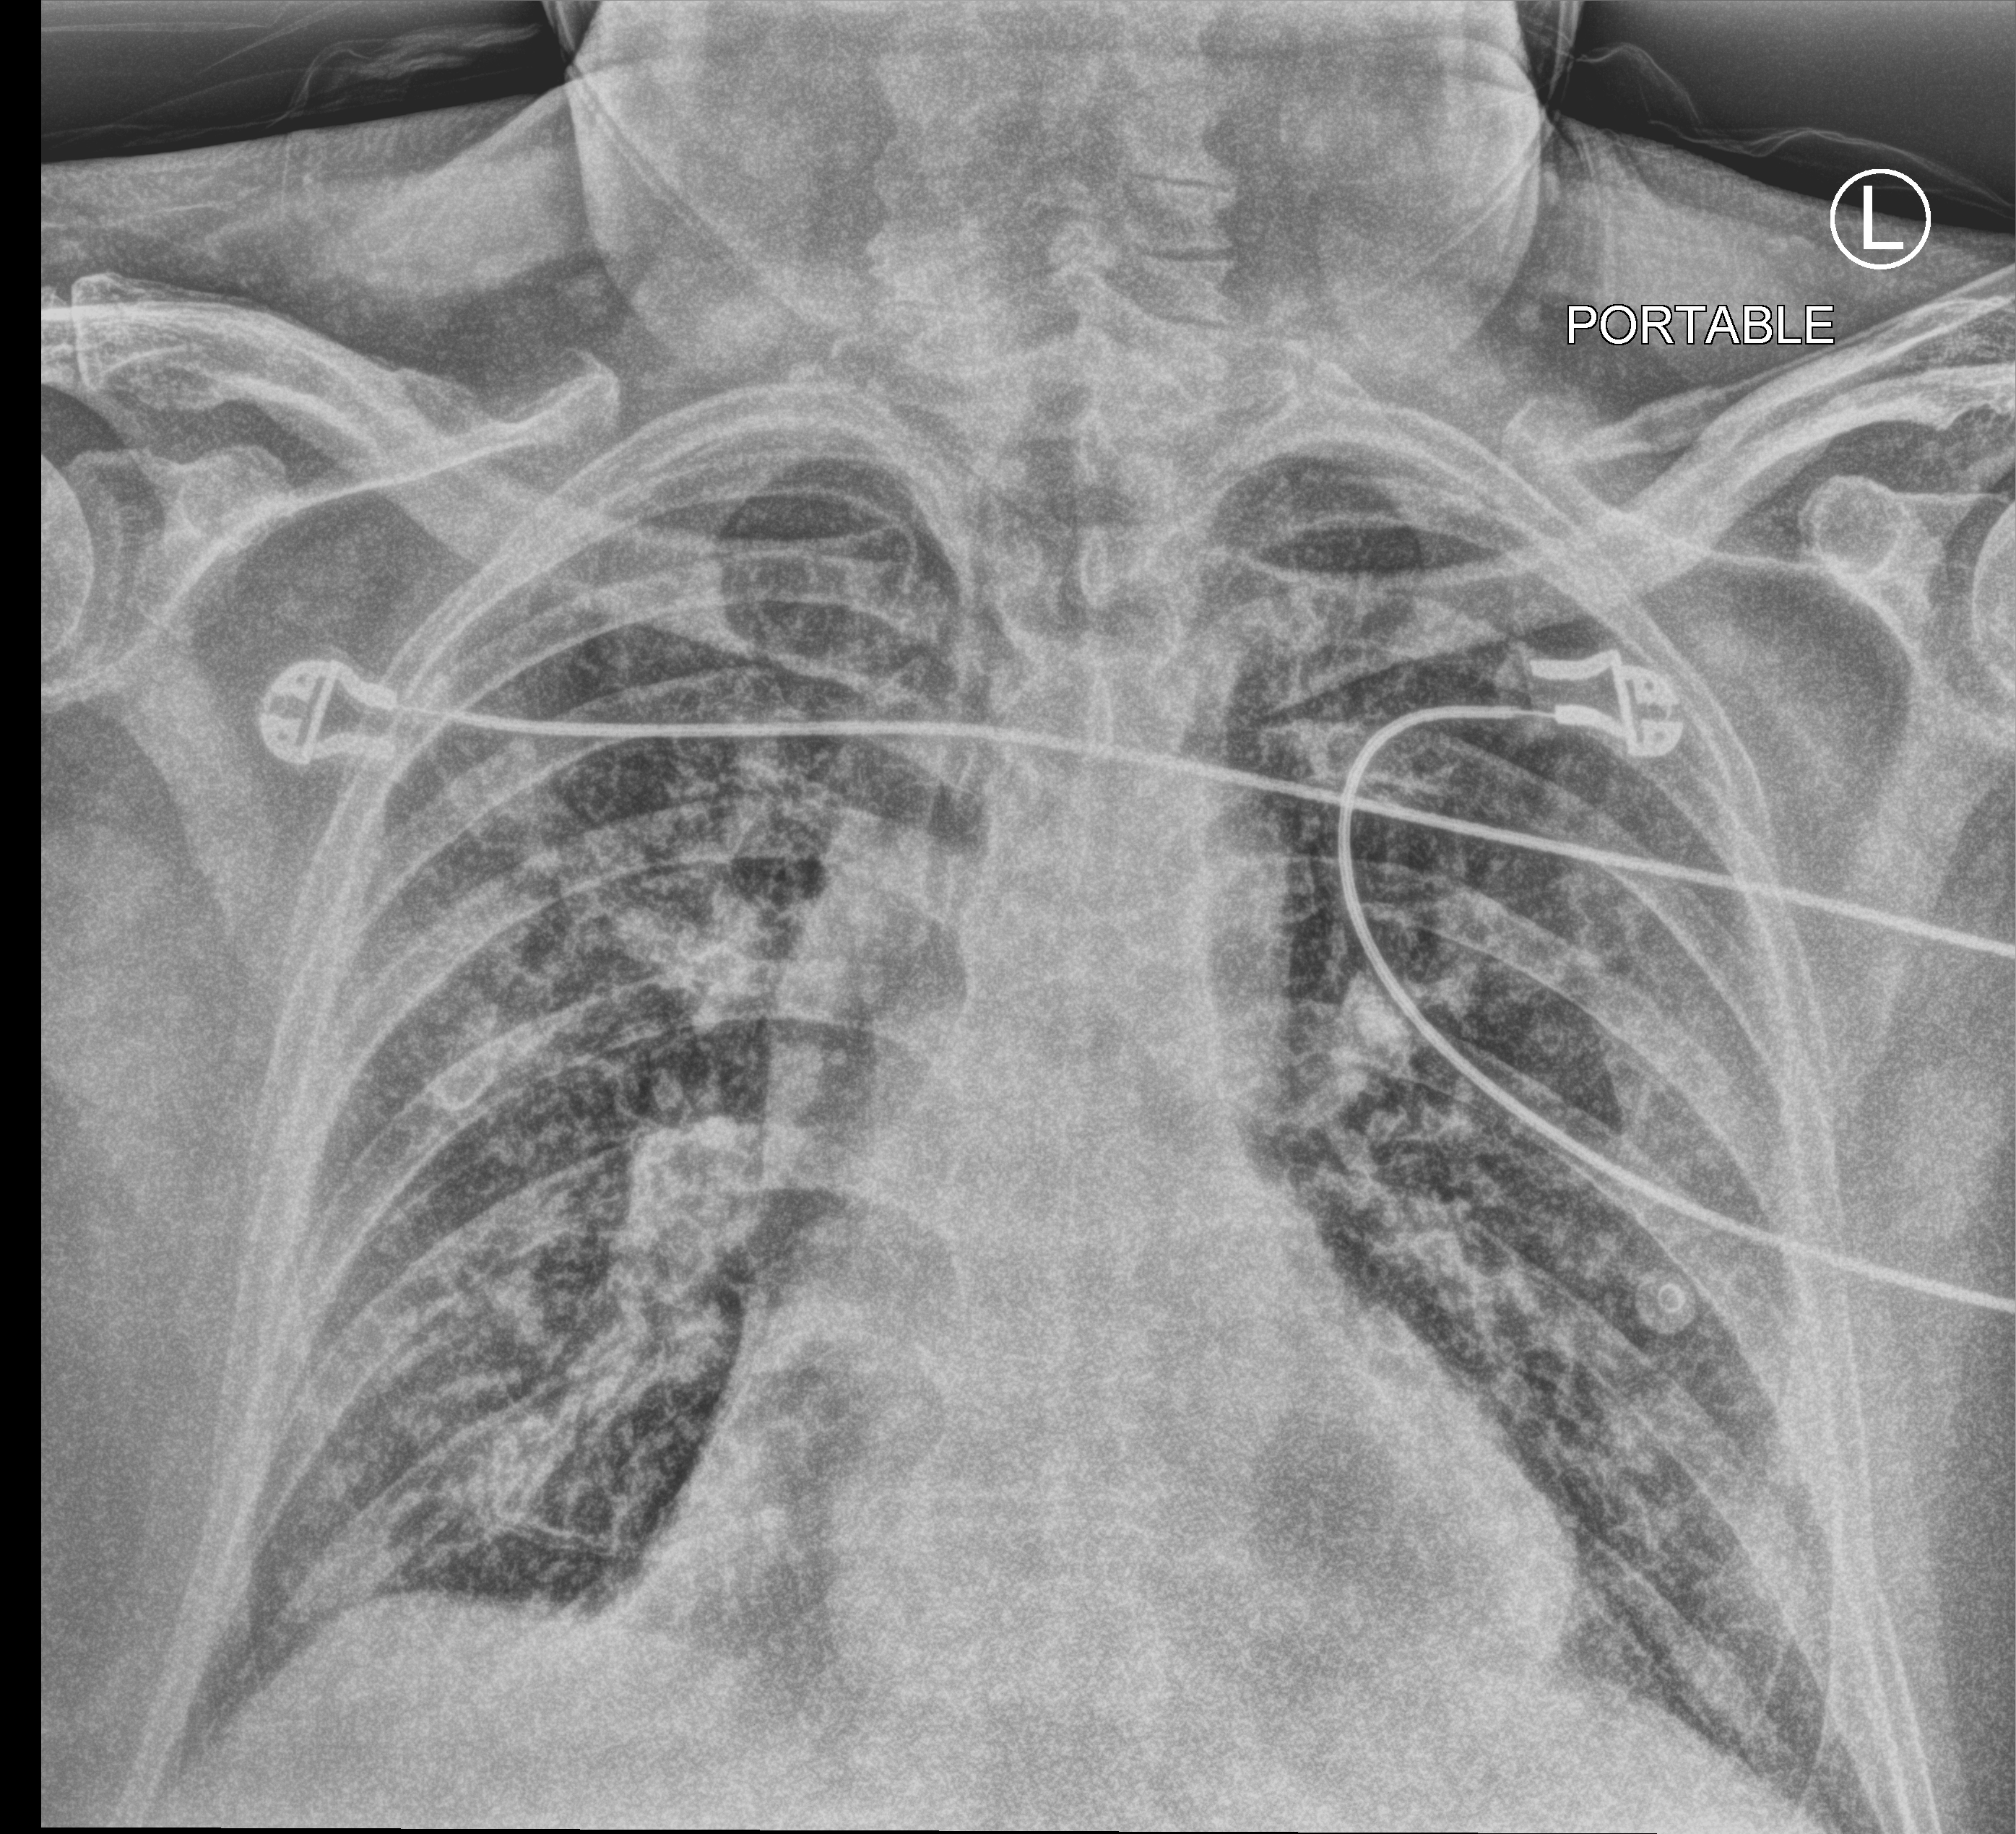
Bedside chest radiograph (computed radiography), anteroposterior (AP) projection. Male patient hospitalised with COVID-19, age 75–90 years.
From the hospital-stay record, not from the radiograph (when in the stay this image was taken is not recorded): length of hospital stay: 14 days; hypertension (admission record): yes; admitted to intensive care during this hospital stay: yes.